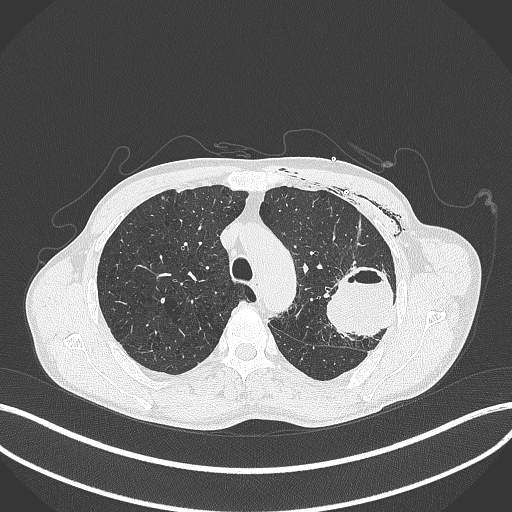
Chest CT, one axial slice. Lung window (W 1500 / L -600 HU). 1 mm slice thickness. 512 × 512 image matrix. Patient: male, 58 years. Case-level facts recorded for this patient, not image findings: clinical TNM (as recorded): T3 N0 M0.
Structures marked on this image (bounding box drawn by a radiologist):
- lung tumour (recorded histology: adenocarcinoma): bounding box <329,262,397,344> (left, top, right, bottom; pixels)